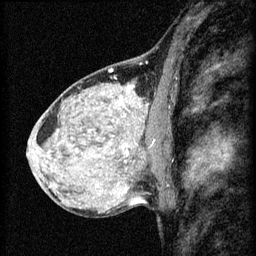
Breast MRI (dynamic contrast-enhanced), one sagittal slice. Slice 36 of 60 in the series (ordered by position). 3 images stored at this slice position (order not interpretable as contrast timing). 1.5 T. TE 4.2 ms, TR 8.2 ms. 2 mm slice thickness. 256 × 256 image matrix, field of view 180 × 180 mm. Patient: female, 40 years.
Outlined on this slice (semi-automatic segmentation, software-assisted and operator-edited):
- analysis volume of interest (the breast-tissue region the enhancement analysis was run in; not a lesion): bounding box <108,108,167,159> (left, top, right, bottom; pixels)
- tumour enhancement mask (voxels above the 70 % enhancement threshold inside the analysis volume of interest): <122,140,155,155>